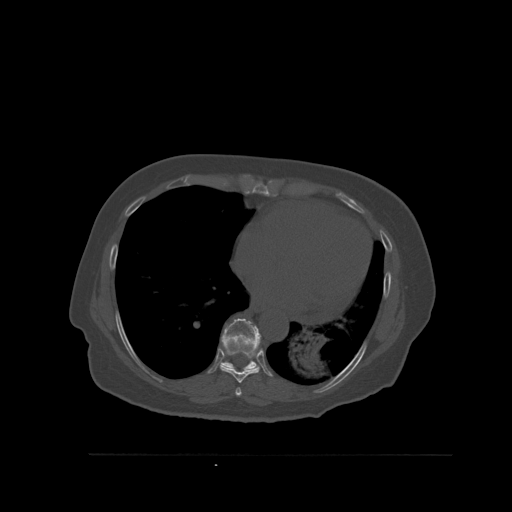
CT including the spine, one axial slice. Bone window (W 1800 / L 400 HU). 1.5 mm slice thickness. 512 × 512 image matrix, field of view 470 × 470 mm. Female patient, age 73 years. From the clinical record (not read from this slice): primary cancer: breast.
Structures marked on this image (semi-automatically segmented with operator editing):
- T7 vertebra: box from (x=235, y=388) to (x=242, y=396) px
- T8 vertebra: (x=220, y=352)–(x=260, y=383)
- T9 vertebra: (x=221, y=318)–(x=261, y=371)